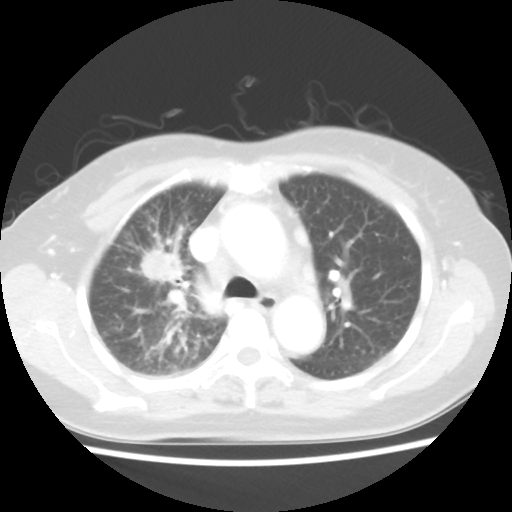
Chest CT, one axial slice. Reconstruction kernel STANDARD. 100 kVp. Lung window (W 1500 / L -600 HU). 512 × 512 image matrix, field of view 312 × 312 mm. Female patient, age 55 years. Case-level facts recorded for this patient, not image findings: clinical TNM (as recorded): T1b N3 M1a.
Outlined on this slice (bounding box drawn by a radiologist):
- lung tumour (recorded histology: adenocarcinoma): bounding box [x1, y1, x2, y2] px = [144, 248, 181, 283]